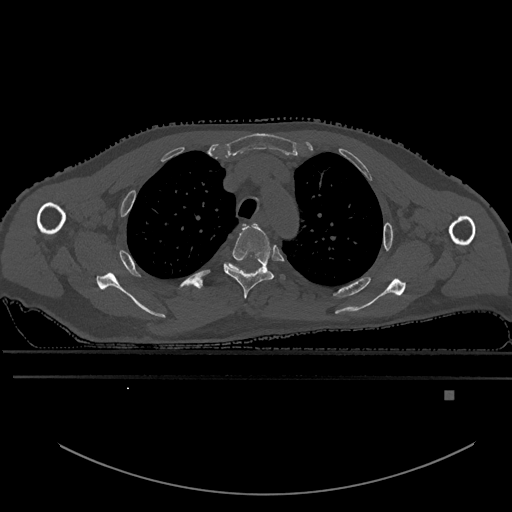
CT including the spine, one axial slice. Position 447 of 969 along the scan axis. Bone window (W 1800 / L 400 HU). 512 × 512 image matrix, field of view 456 × 456 mm. Patient: male, 82 years. From the clinical record (not read from this slice): primary cancer: prostate.
Structures marked on this image (semi-automatic segmentation, software-assisted and operator-edited):
- T3 vertebra: bounding box [x1, y1, x2, y2] px = [223, 224, 285, 299]
- T4 vertebra: [227, 263, 260, 270]